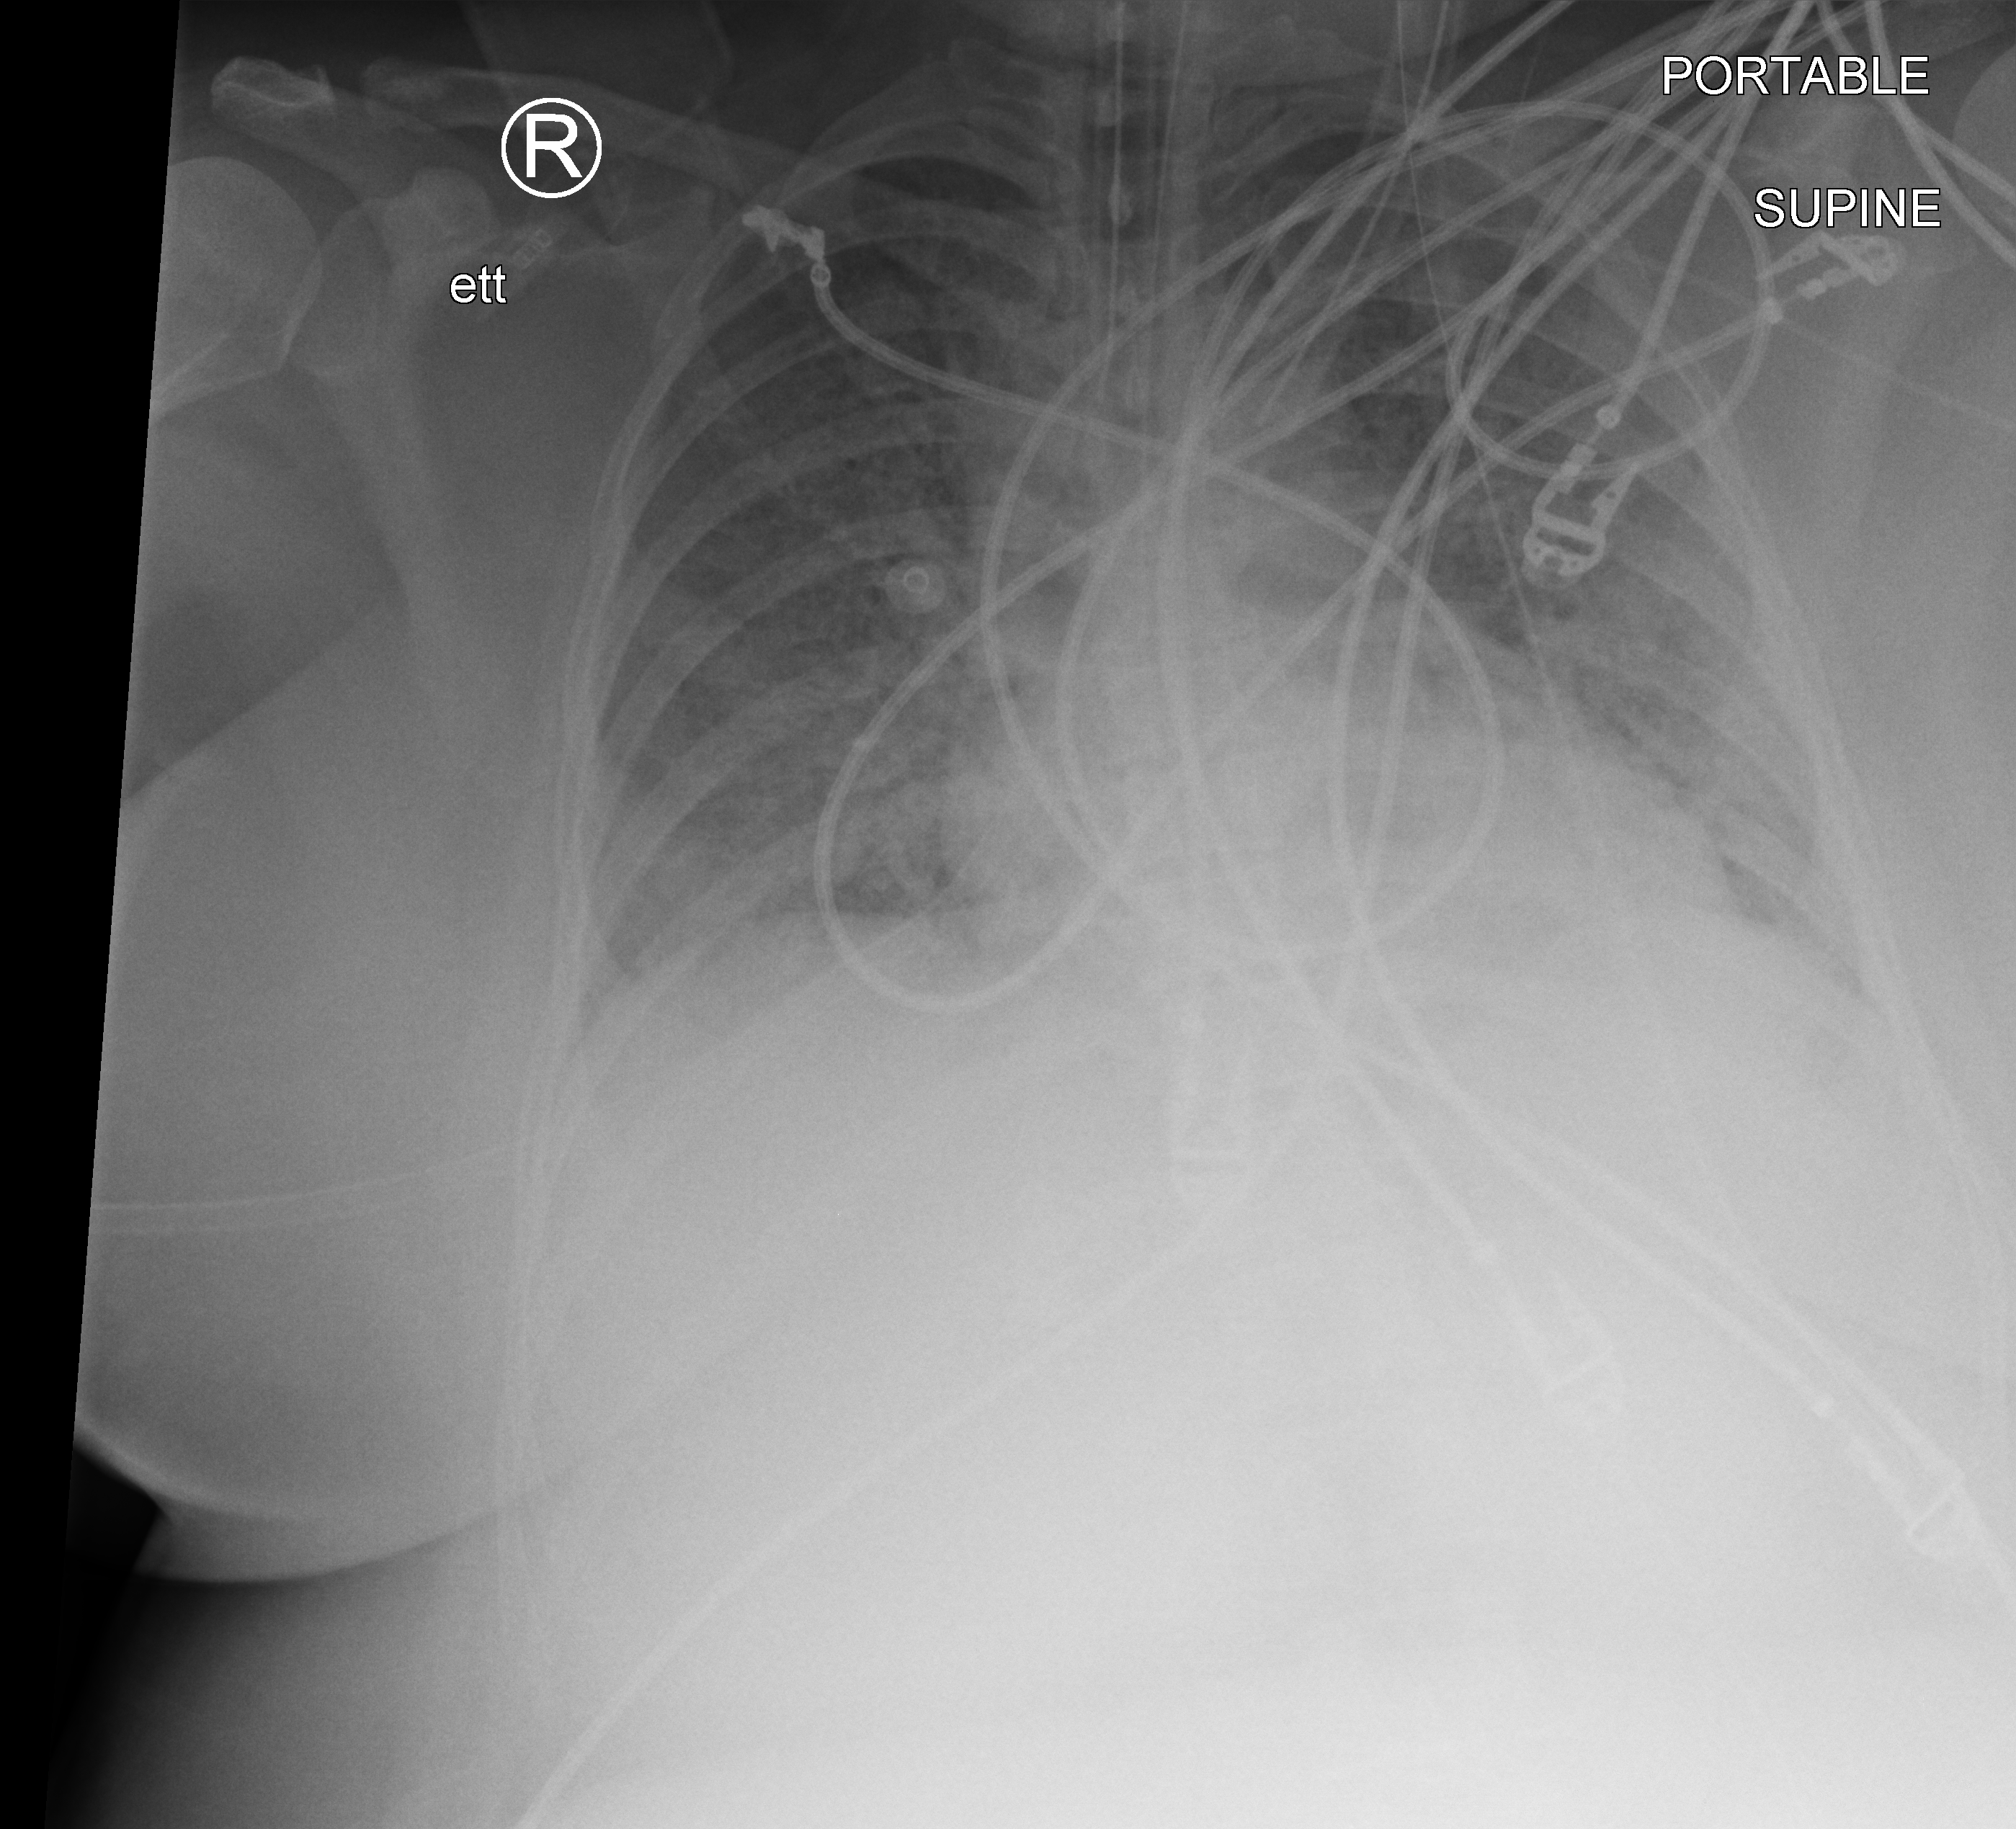
Bedside chest radiograph (computed radiography). Female patient hospitalised with COVID-19, age 18–59 years.
From the hospital-stay record, not from the radiograph (when in the stay this image was taken is not recorded): admitted to intensive care during this hospital stay: yes; other chronic lung disease (admission record): no.